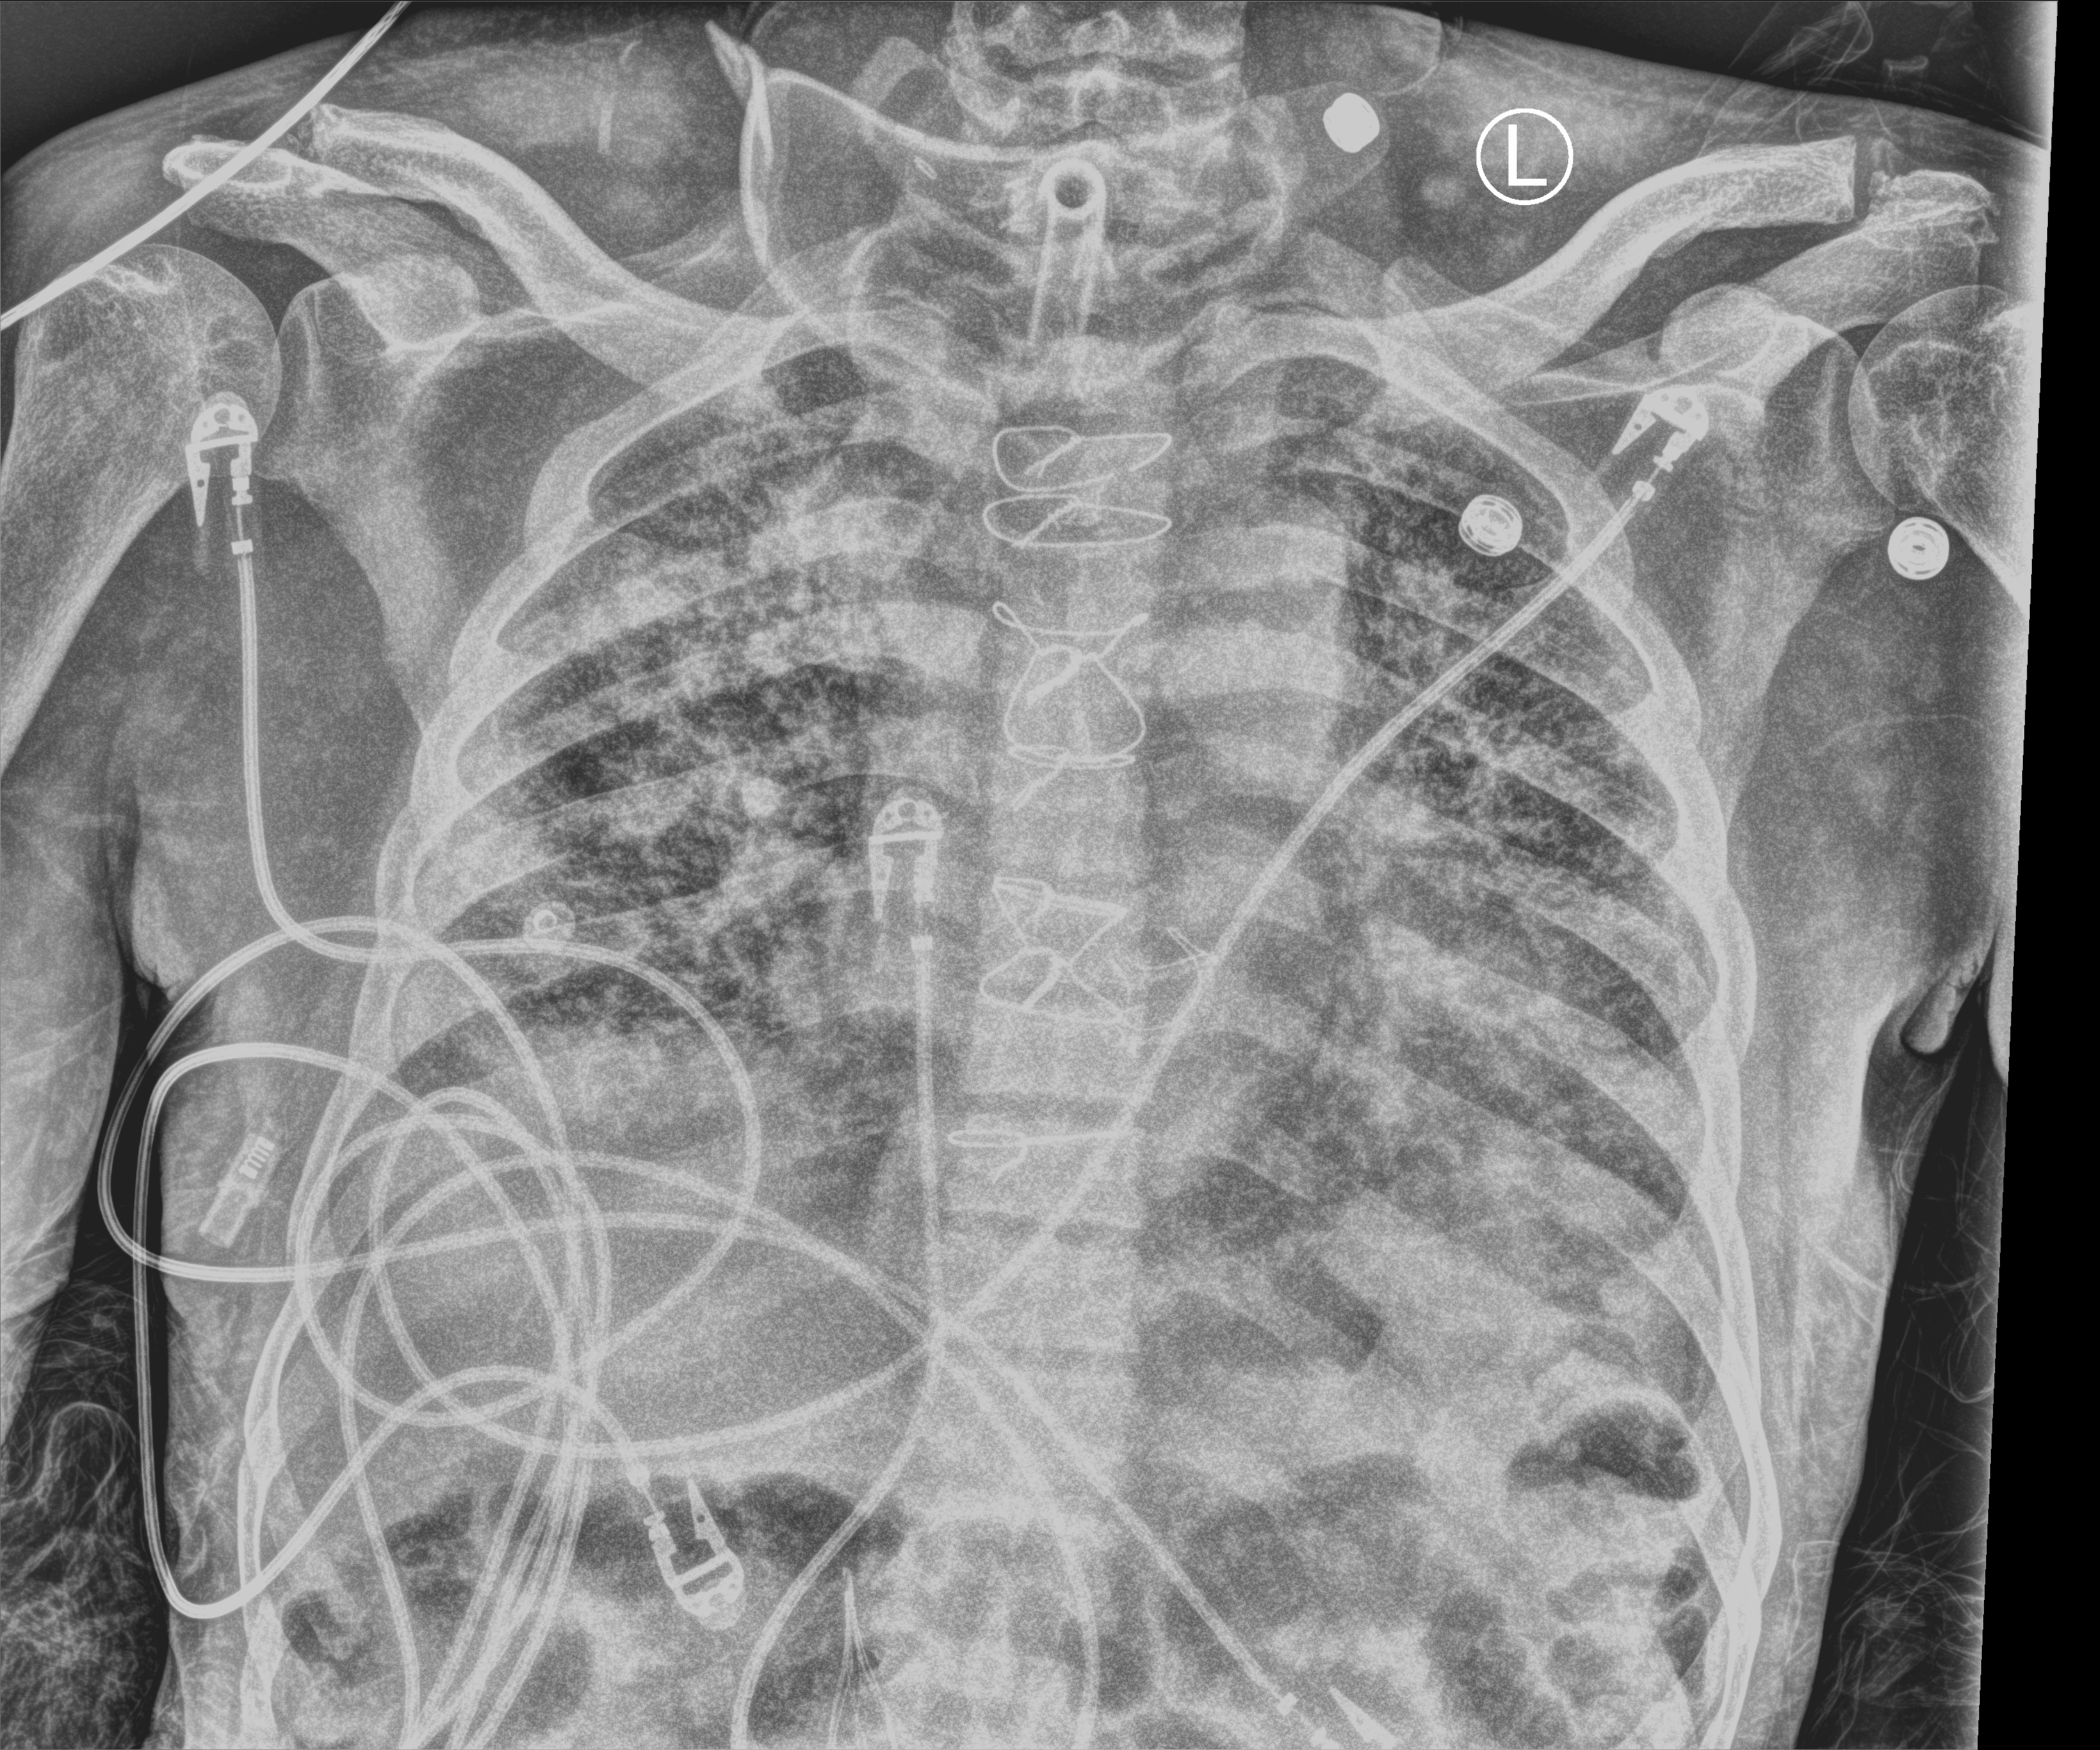
Bedside chest radiograph (computed radiography), anteroposterior (AP) projection. Patient hospitalised with COVID-19; male, aged 60–74 years.
Hospital-stay facts (about this admission, not read from this image; timing relative to this image not recorded):
- COPD (admission record): no
- admitted to intensive care during this hospital stay: yes
- other chronic lung disease (admission record): no